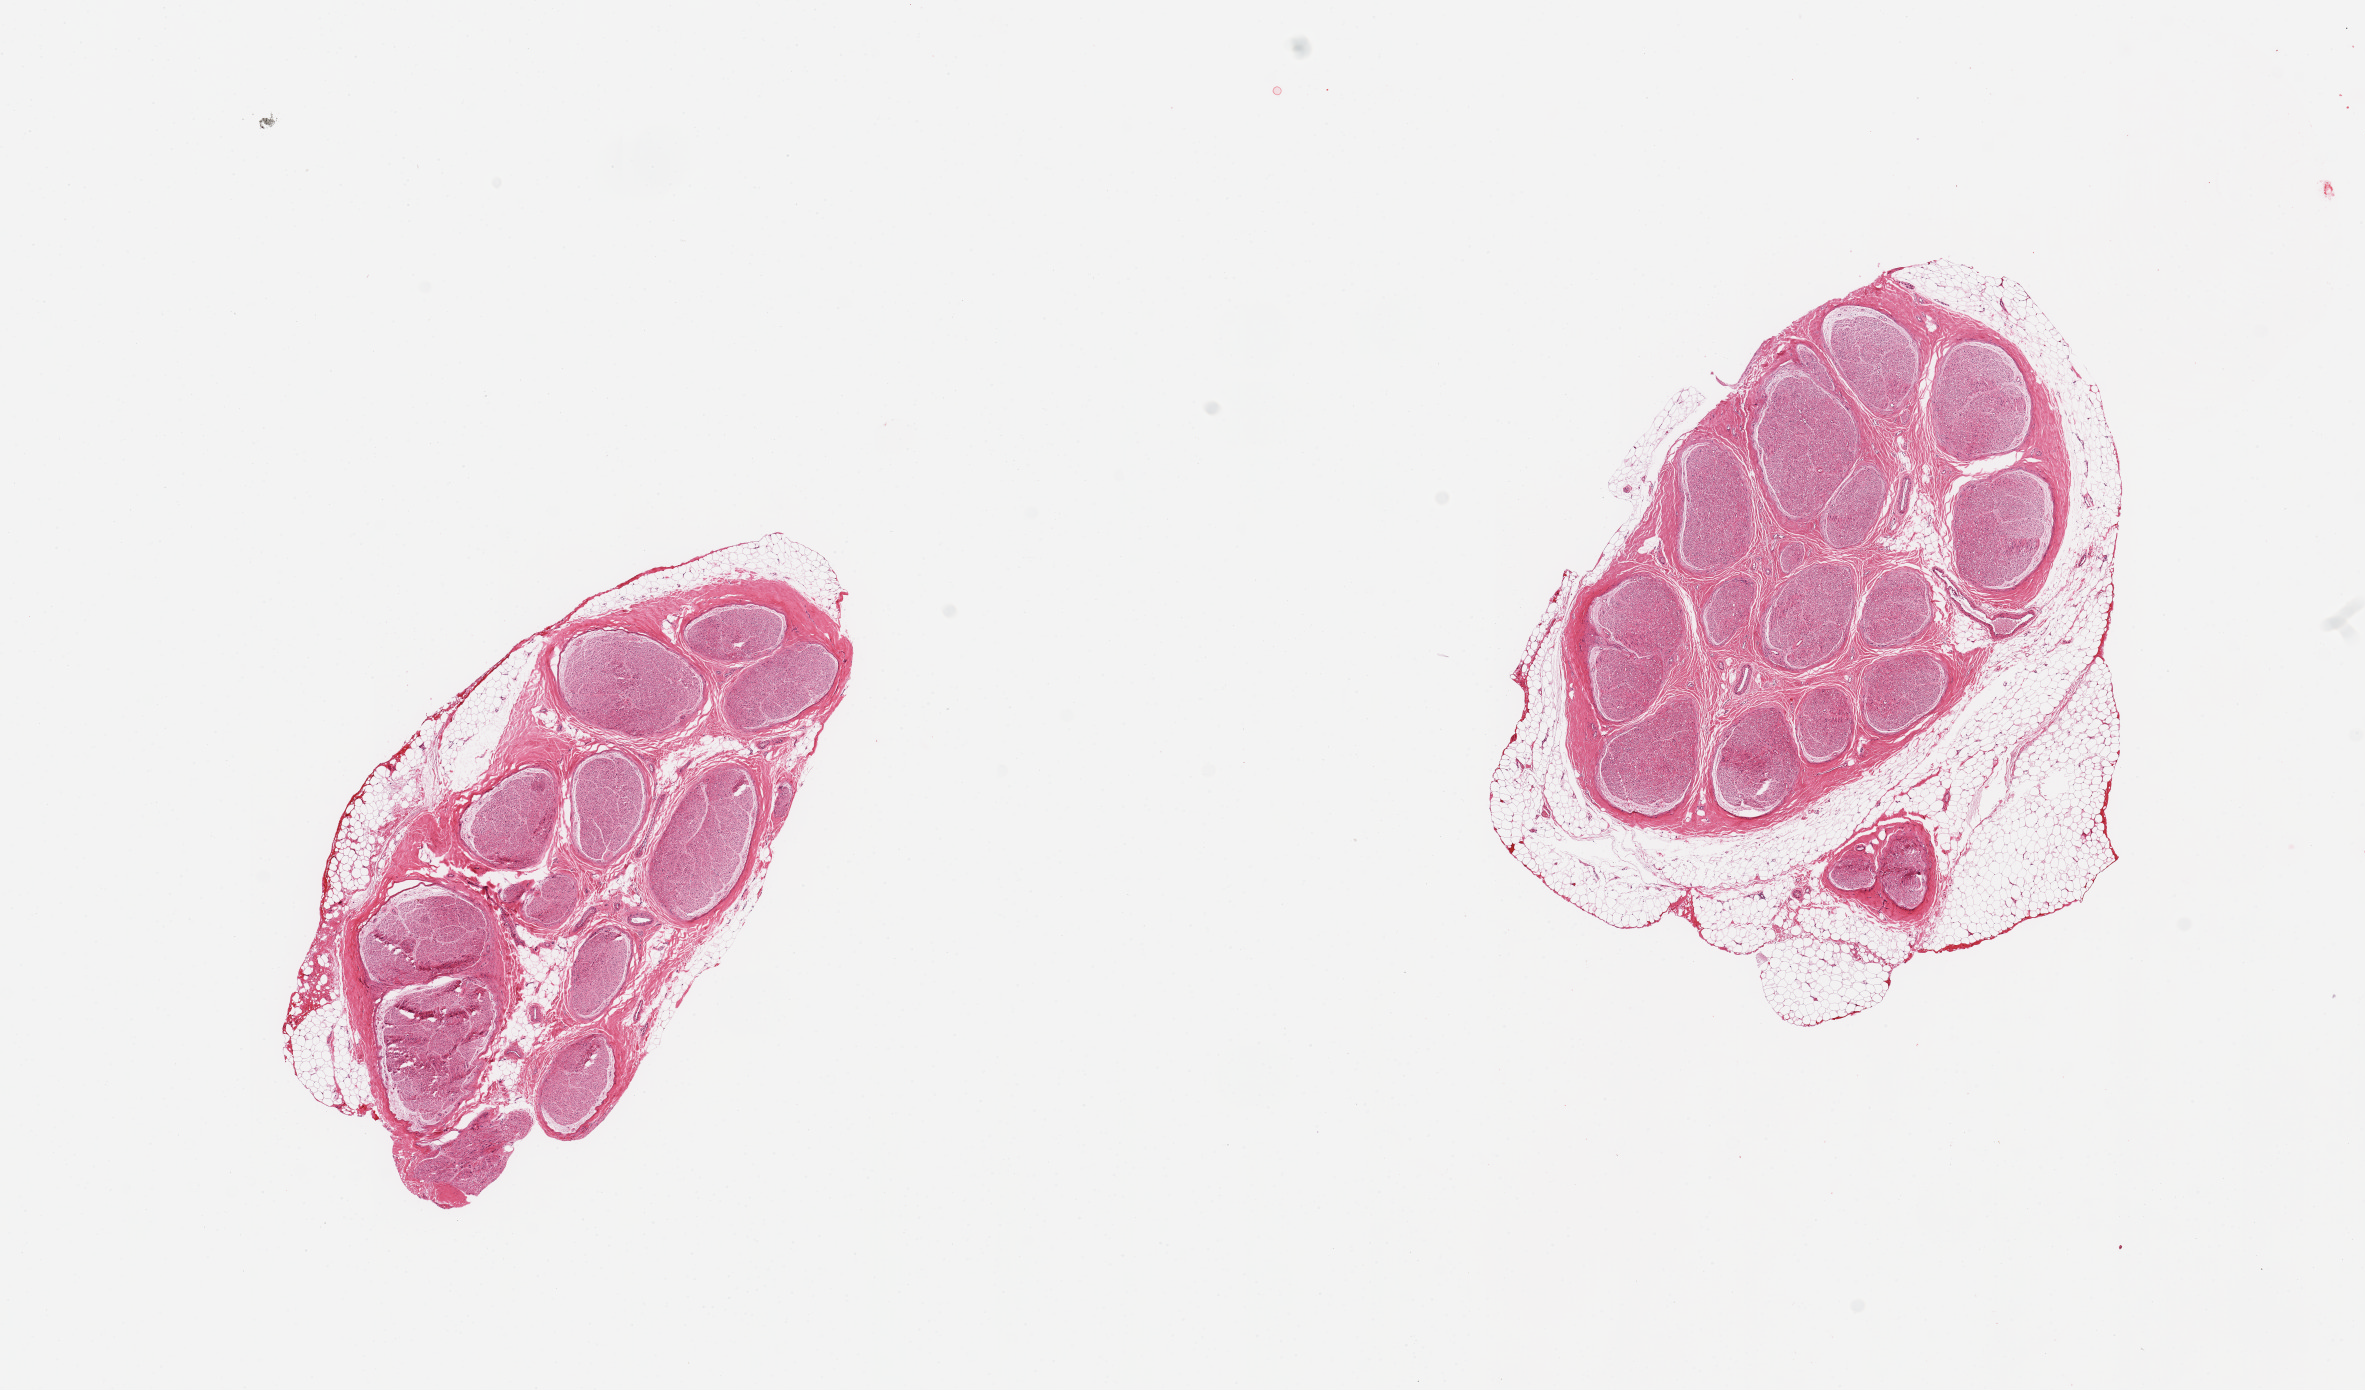
Digitized H&E-stained section — whole scanned area (about 18.7 x 11.0 mm, acquisition: 20x scan) shown as a low-resolution overview. PAXgene-fixed paraffin-embedded (PFPE) section. Section of tibial nerve (target tissue). Donor tissue sample. Male donor.
Review note (as recorded): 2 pieces; include 20 and 40% attached and internal fat.